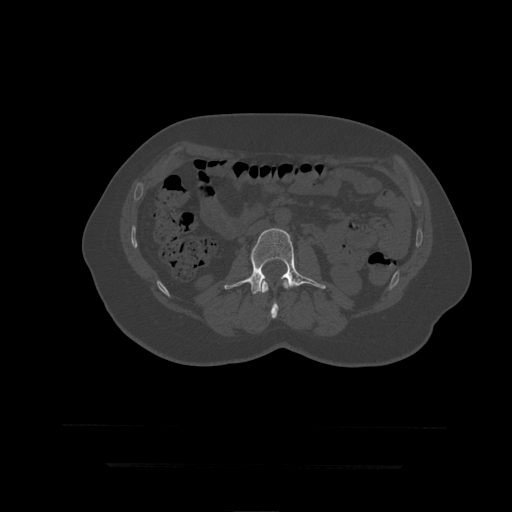
CT including the spine, one axial slice. Position 130 of 399 along the scan axis. 120 kVp. Bone window (W 1800 / L 400 HU). 512 × 512 image matrix, field of view 450 × 450 mm. Patient age 41 years. From the clinical record (not read from this slice): primary cancer: breast.
Outlined on this slice (semi-automatic segmentation, software-assisted and operator-edited):
- L2 vertebra: bounding box (x1, y1, x2, y2) in pixels: (262, 280, 289, 319)
- L3 vertebra: (225, 229, 326, 294)